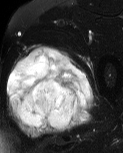
MRI of an extremity soft-tissue mass, one axial slice; T2-weighted fat-saturated; MR volume resampled by the dataset authors to the PET/CT grid (not the native acquisition matrix); 123 × 153 image matrix. Male patient. From the clinical record (not read from this slice): histological type: pleiomorphic liposarcoma; grade: high; site of the primary tumour: left thigh.
Annotated regions visible in this slice (expert contour drawn on MRI and transferred to this co-registered scan by the dataset authors):
- gross tumour volume including surrounding oedema: bounding box <6,45,94,139> (left, top, right, bottom; pixels)
- gross tumour volume (mass): <6,47,92,130>